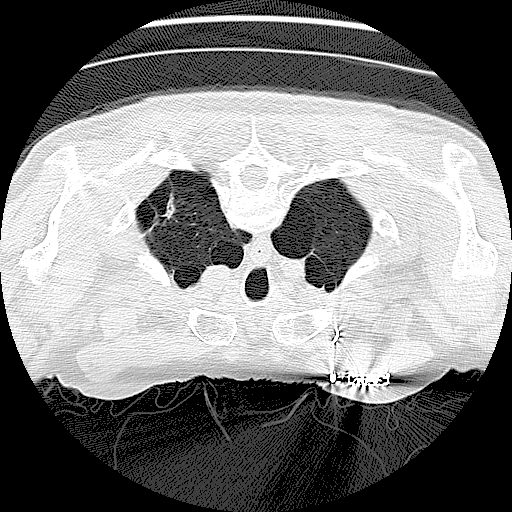
Low-dose screening chest CT, one axial slice. Position 121 of 138 along the scan axis. Reconstruction kernel LUNG. 120 kVp. Lung window (W 1500 / L -600 HU). 2.5 mm slice thickness. 512 × 512 image matrix, field of view 330 × 330 mm.
Structures marked on this image (expert manual segmentation):
- lesion 1 (tumor): box from (x=157, y=193) to (x=179, y=223) px